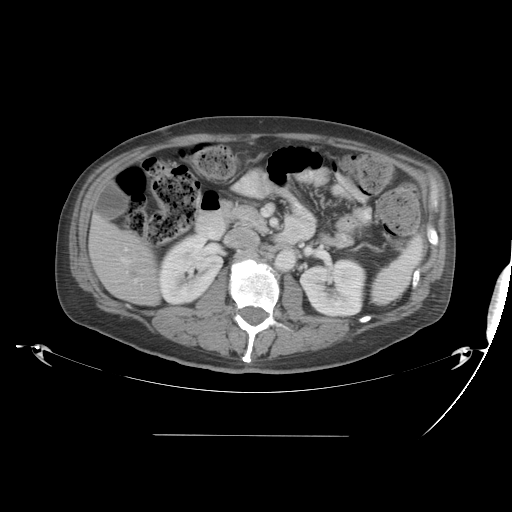
Contrast-enhanced abdominal CT, one axial slice. Position 17 of 48 along the scan axis. Reconstruction kernel STANDARD. Intravenous contrast given. Soft-tissue window (W 400 / L 40 HU). 5 mm slice thickness. 512 × 512 image matrix. Male patient, age 65 years. From the clinical record (not read from this slice): diagnosis: colorectal cancer liver metastases, imaged before liver resection; multiple liver metastases: yes; largest metastasis: 11 cm.
Outlined on this slice (manually delineated by an expert):
- hepatic veins: box from (x=122, y=259) to (x=127, y=262) px
- liver: (x=90, y=218)–(x=161, y=305)
- portal vein (with intrahepatic branches): (x=134, y=279)–(x=138, y=283)
- liver metastasis: (x=128, y=269)–(x=136, y=278)